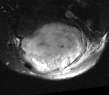
MRI of an extremity soft-tissue mass, one axial slice. Position 22 of 52 along the scan axis. T2-weighted fat-saturated. MR volume resampled by the dataset authors to the PET/CT grid (not the native acquisition matrix). 109 × 95 image matrix. Male patient. From the clinical record (not read from this slice): histological type: synovial sarcoma; site of the primary tumour: left poplietal fossa.
Annotated regions visible in this slice (expert contour drawn on MRI and transferred to this co-registered scan by the dataset authors):
- gross tumour volume (mass): bounding box <17,20,89,75> (left, top, right, bottom; pixels)